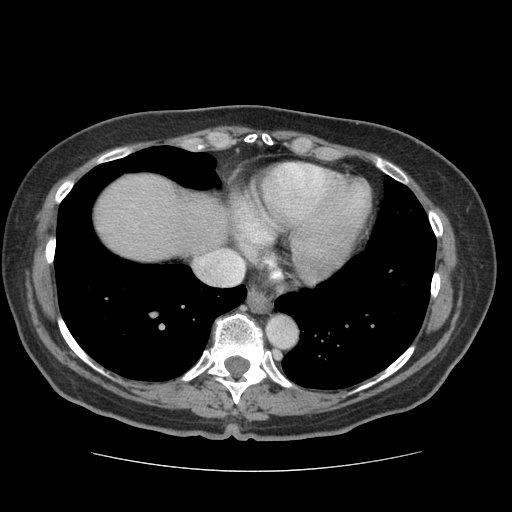
Contrast-enhanced abdominal CT (liver protocol), one axial slice. Position 67 of 75 along the scan axis. Soft-tissue window (W 400 / L 40 HU). 2.5 mm slice thickness. 512 × 512 image matrix. Case-level facts recorded for this patient, not image findings: diagnosis: hepatocellular carcinoma (patient treated with transarterial chemoembolisation; whether this scan precedes or follows treatment is not stated here); TNM stage (as recorded): Stage-I; Child-Pugh class: A; tumour differentiation: moderately differentiated; tumour nodularity: uninodular.
Structures marked on this image (semi-automatic segmentation, software-assisted and operator-edited):
- liver parenchyma outside the tumour (the mass and vessels are separate outlines, so this box may not span the whole liver): bounding box [x1, y1, x2, y2] px = [94, 174, 228, 260]